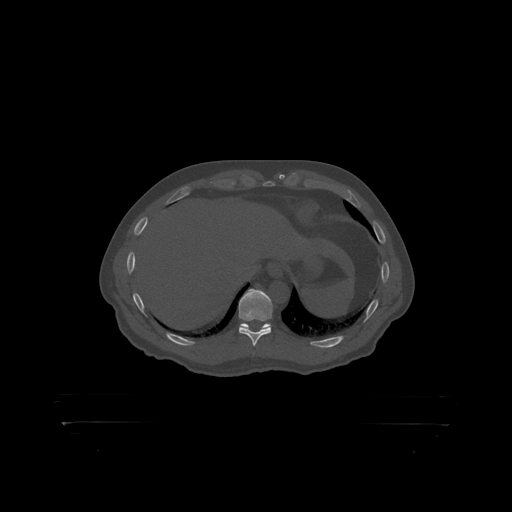
CT including the spine, one axial slice. Slice 395 of 399 in the series (ordered by position). Bone window (W 1800 / L 400 HU). 1.25 mm slice thickness. 512 × 512 image matrix. Male patient, age 46 years. Case-level facts recorded for this patient, not image findings: primary cancer: skin.
Outlined on this slice (semi-automatic segmentation, software-assisted and operator-edited):
- T10 vertebra: bounding box <239,289,273,319> (left, top, right, bottom; pixels)